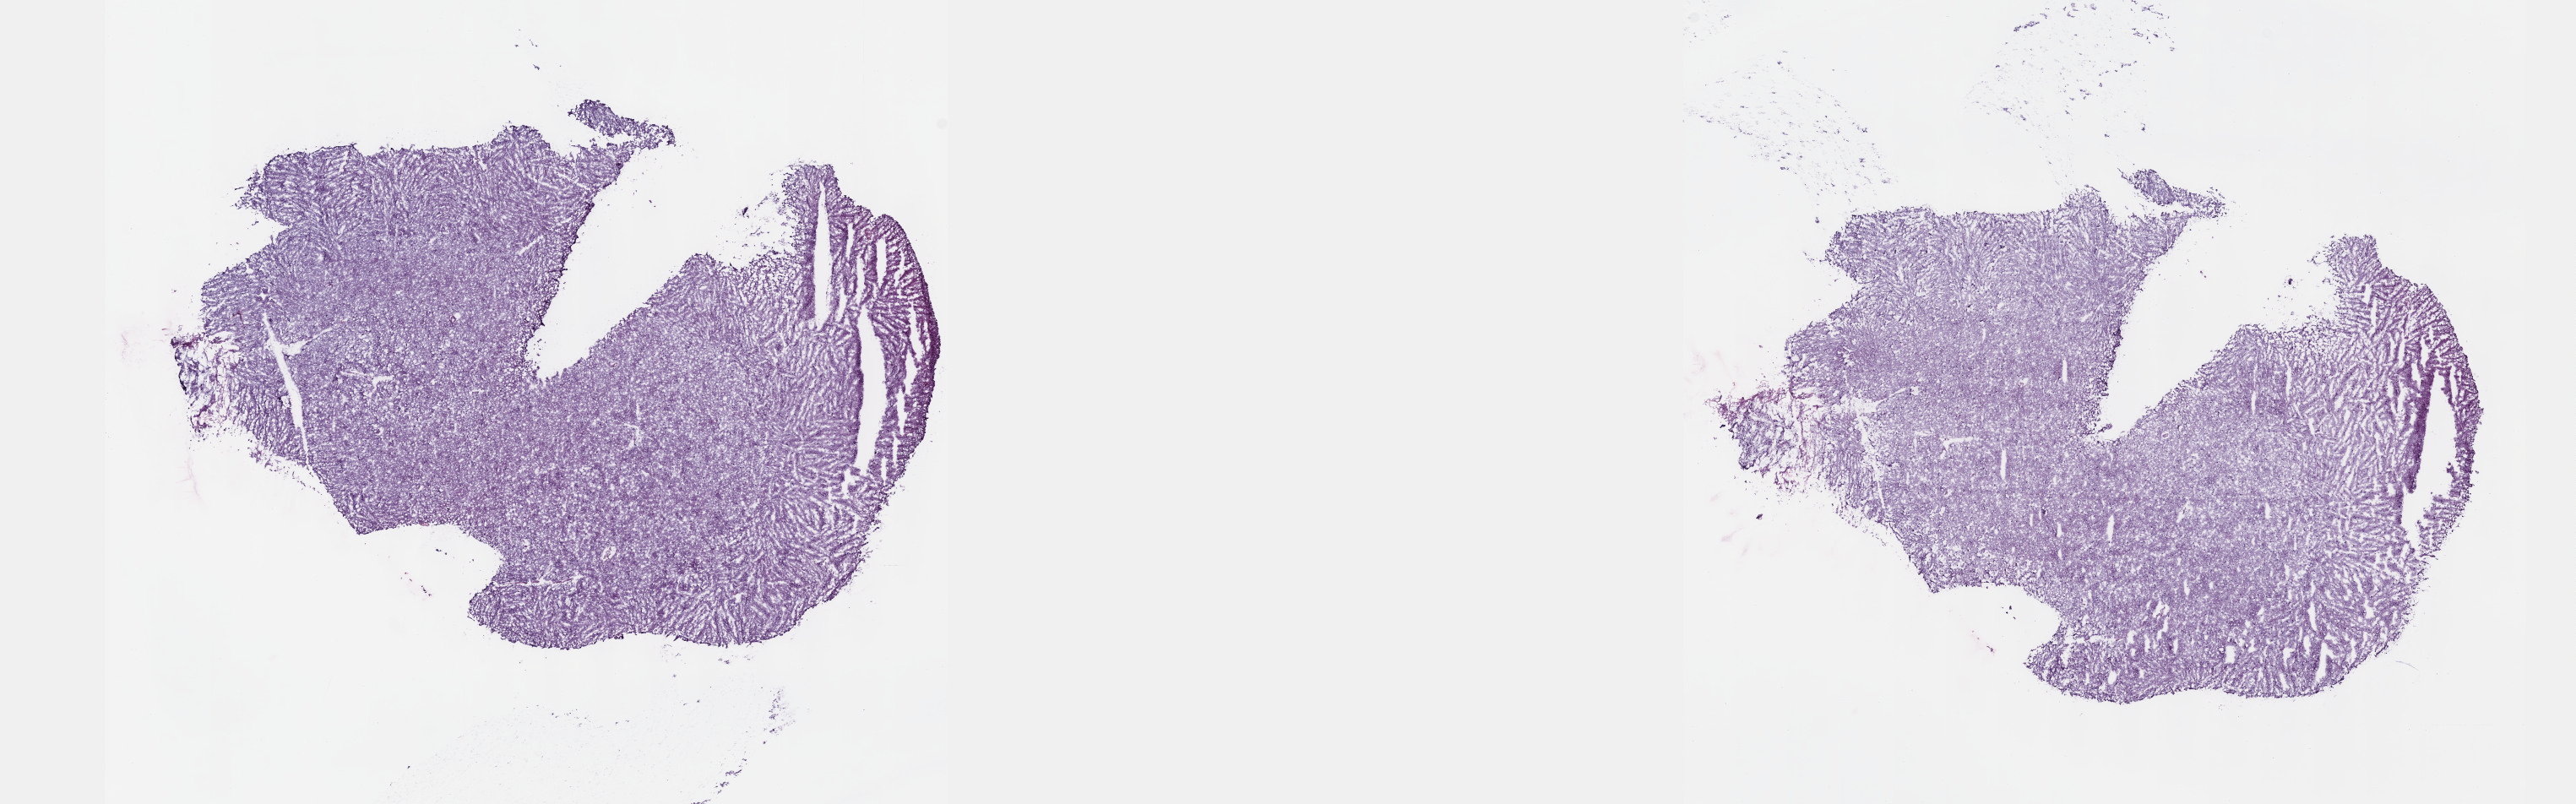
H&E whole-slide image — low-resolution overview of the scanned area, about 24.6 x 7.7 mm (from a 40x scan); frozen section from the top of the tissue portion; brain, primary tumour sample. Male, age 44 years at initial diagnosis.
Histologic diagnosis: Astrocytoma, NOS.